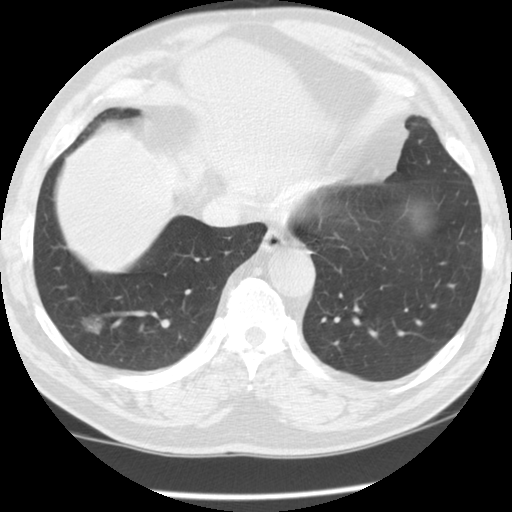
Low-dose screening chest CT, one axial slice; position 28 of 115 along the scan axis; lung window (W 1500 / L -600 HU); 2.5 mm slice thickness; 512 × 512 image matrix.
Annotated regions visible in this slice (outlined manually by an expert reader):
- lesion 1 (tumor, lower lobe of right lung): bounding box [x1, y1, x2, y2] px = [82, 318, 102, 334]